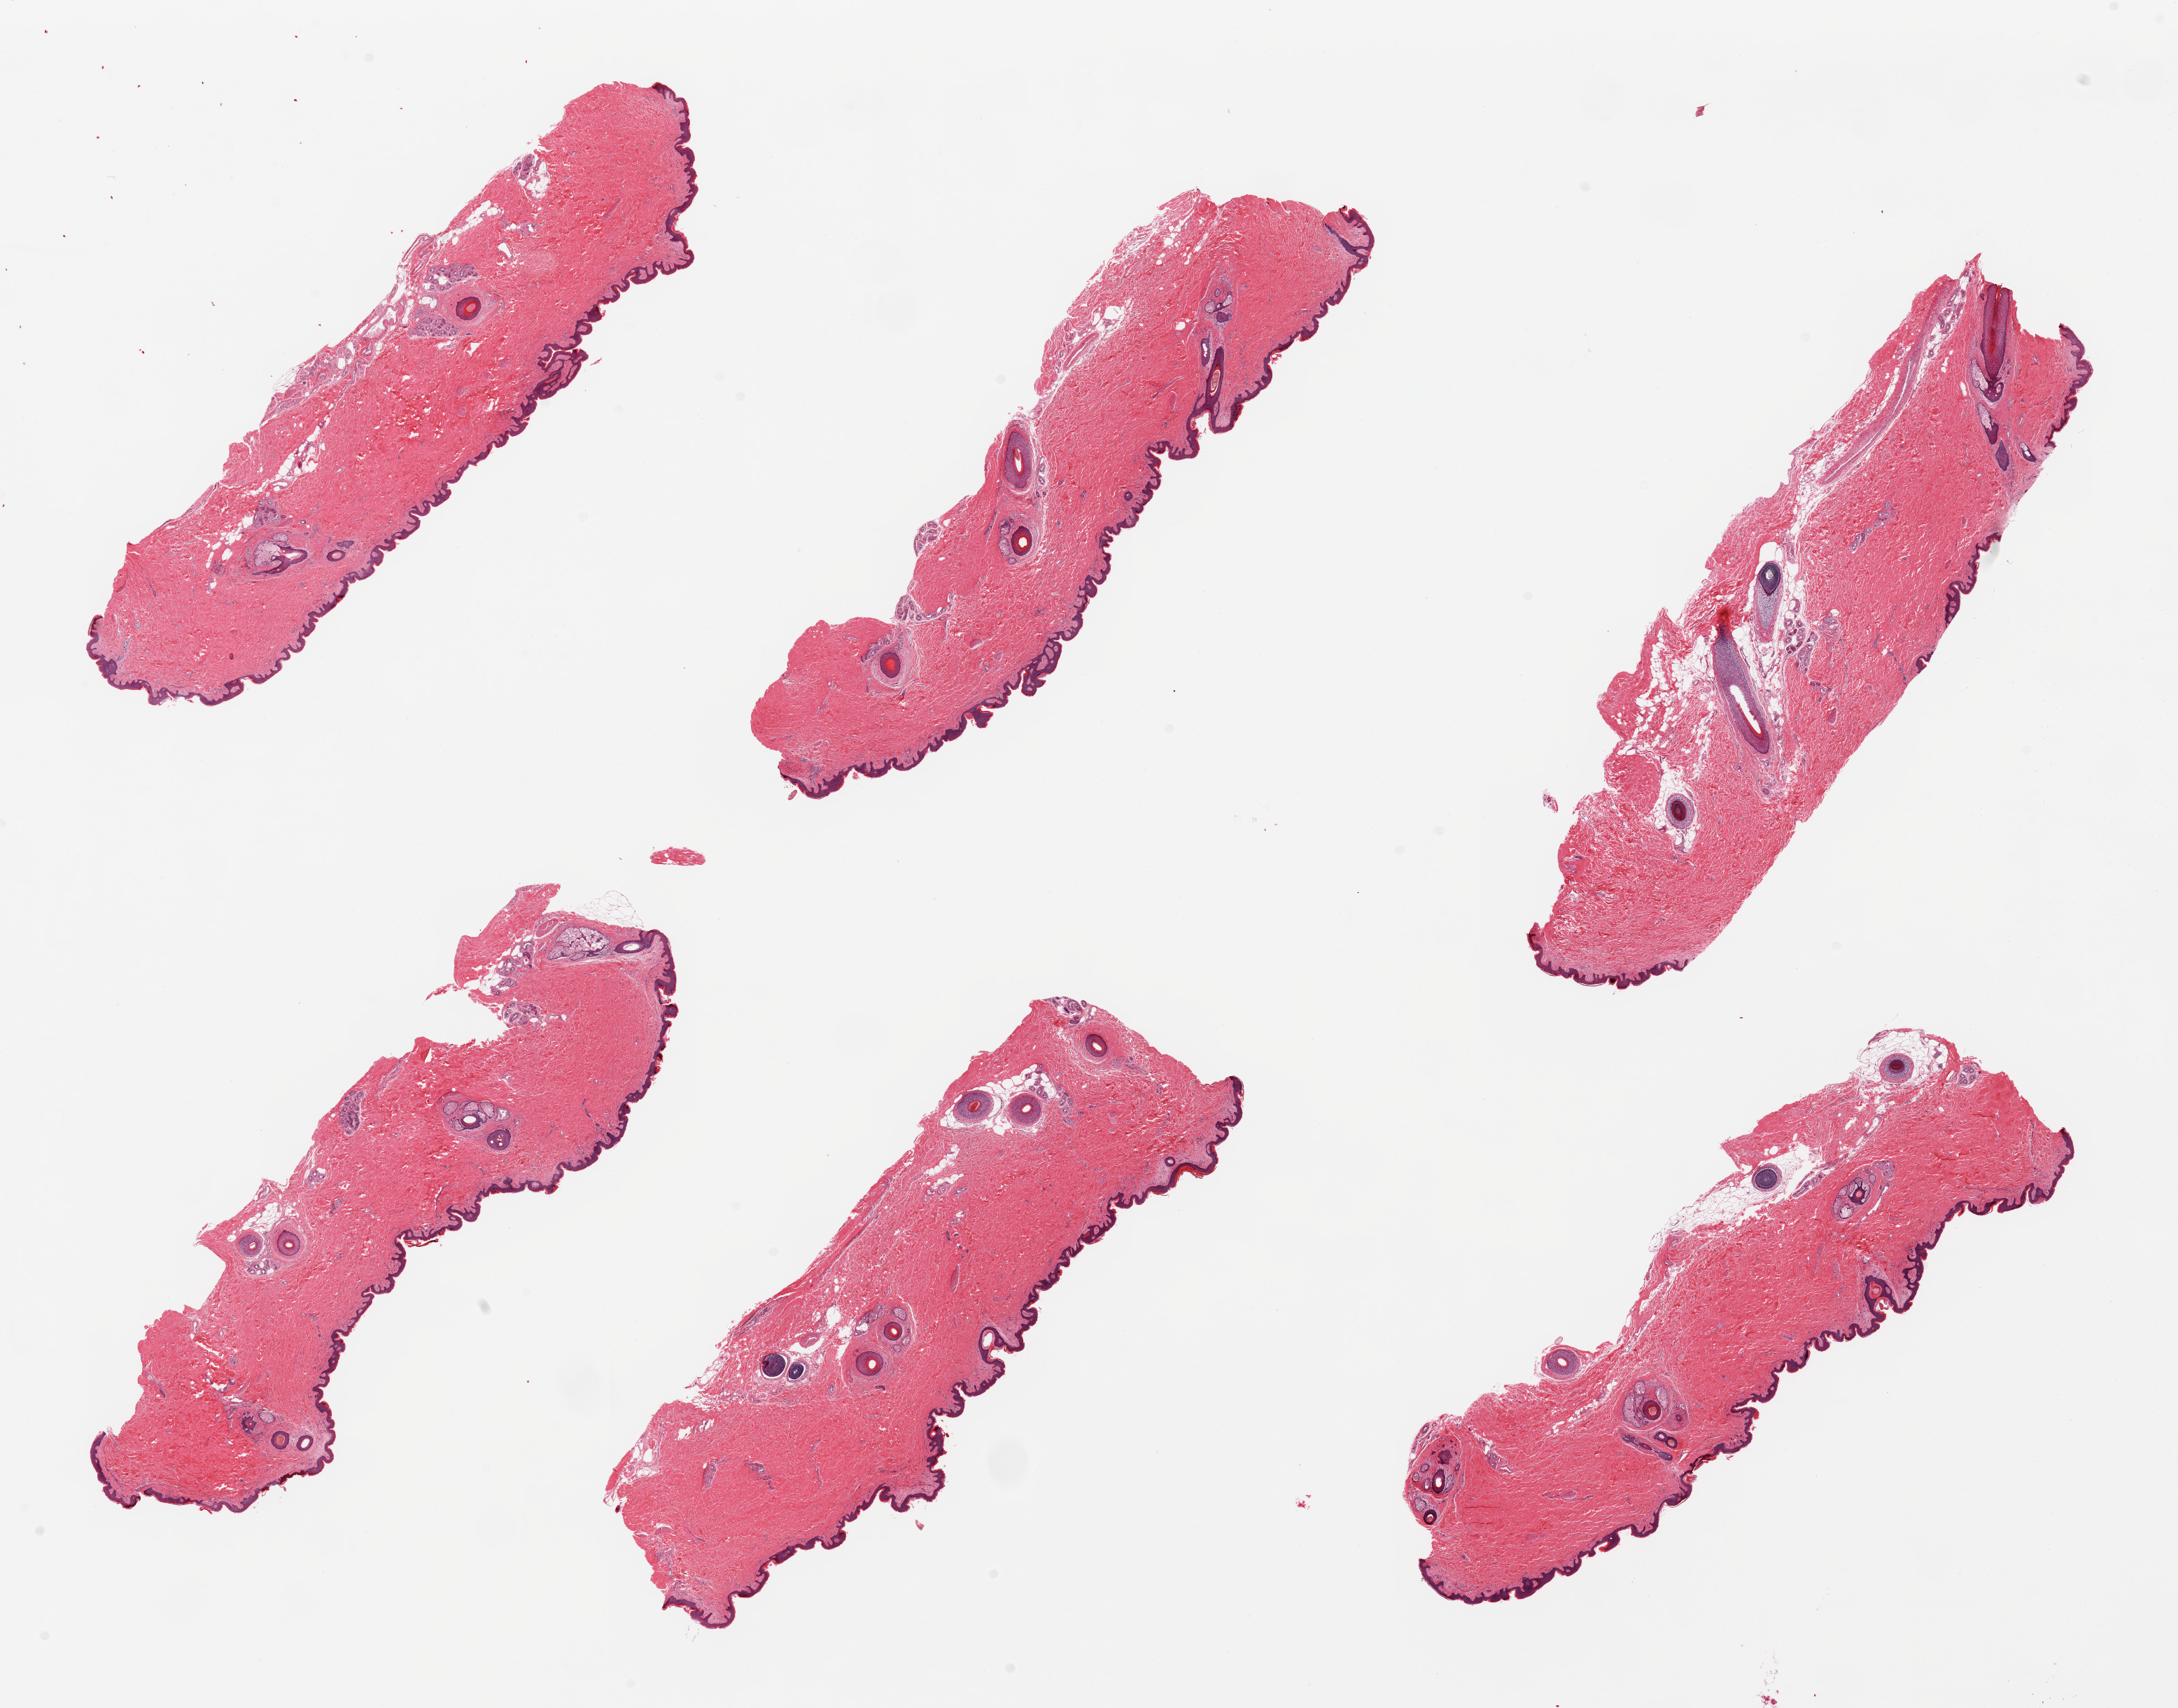
Digitized hematoxylin and eosin (H&E)-stained section — low-resolution overview of the scanned area, about 24.6 x 19.3 mm (from a 20x scan), PAXgene-fixed paraffin-embedded (PFPE) section, target tissue: skin of suprapubic region, tissue donor sample. Donor: male.
Reviewer comment on this tissue sample: 6 pieces; well trimmed.